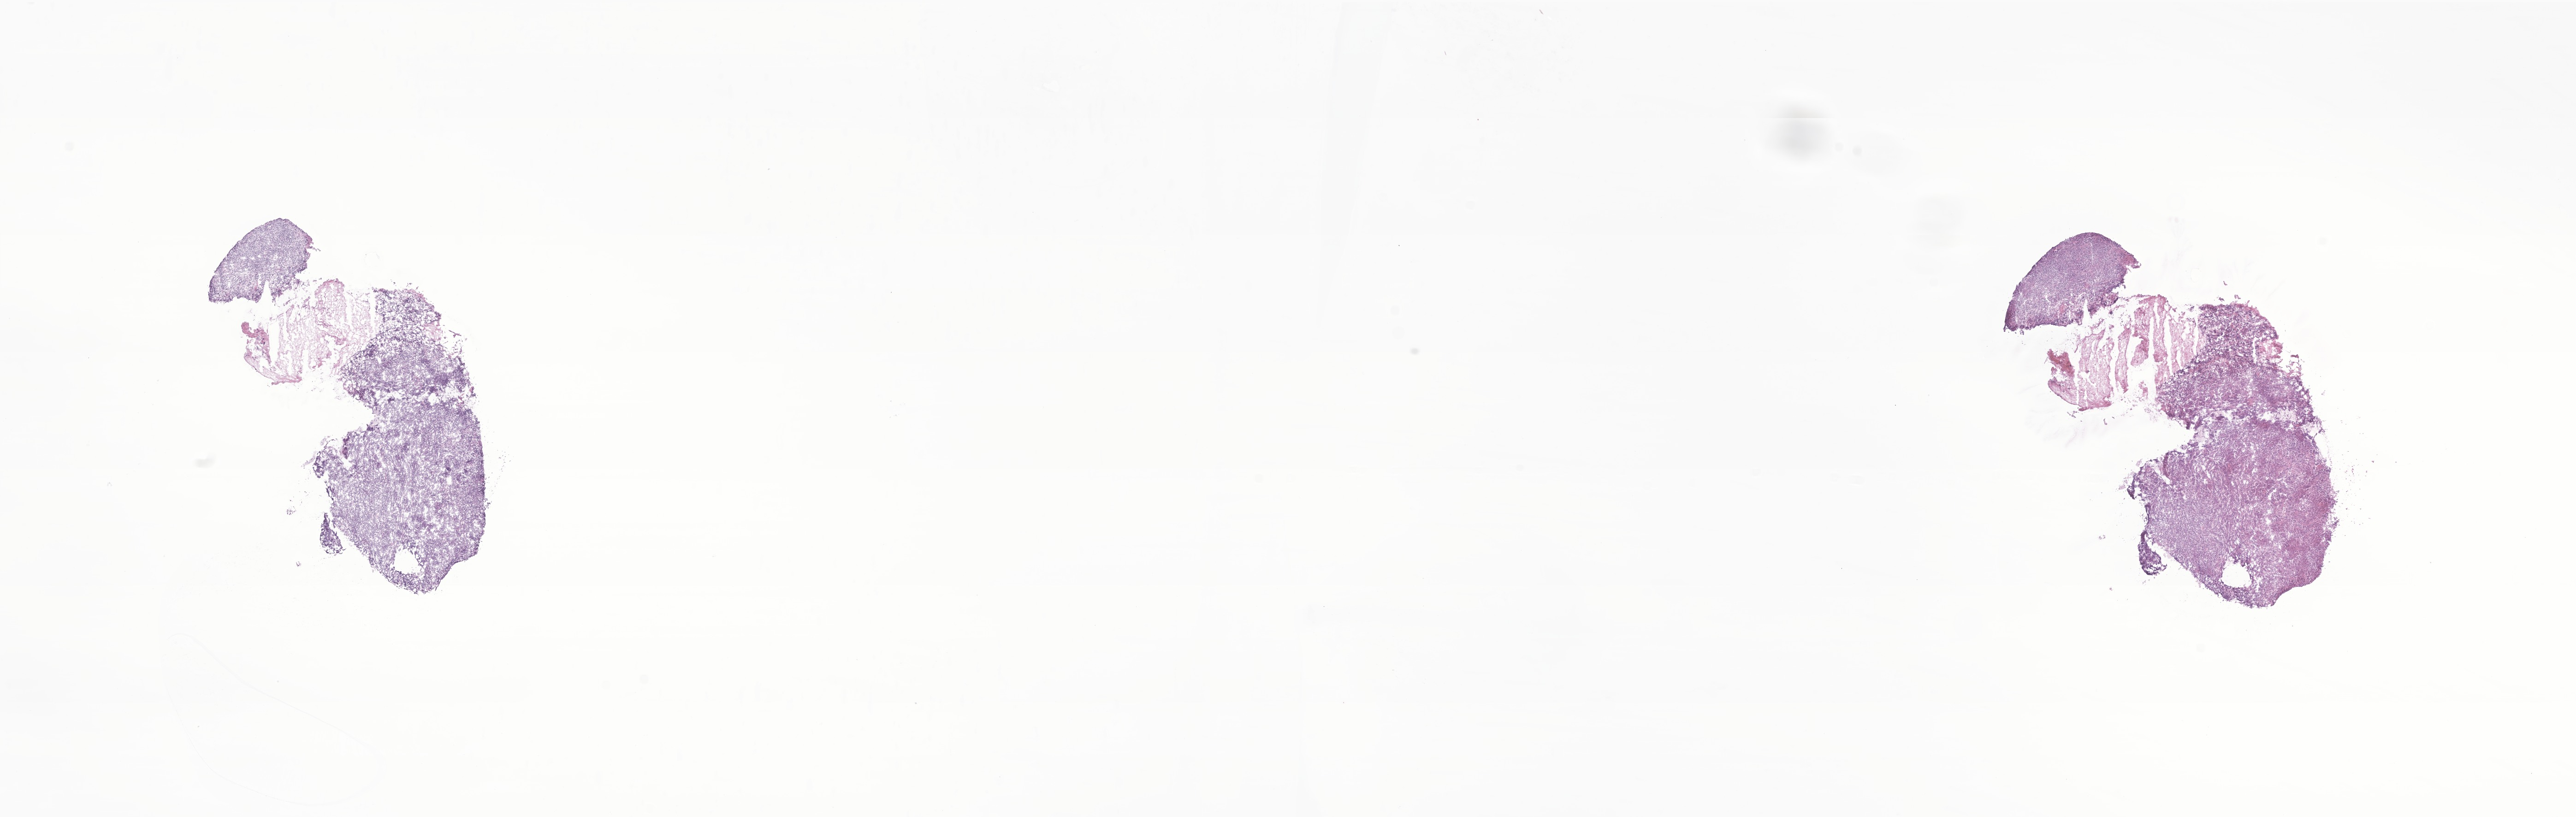
Digitized H&E-stained section of tumor tissue from the brain, shown as a low-resolution overview of the whole scanned area (about 23.6 x 7.5 mm); cryosection (OCT / tissue freezing medium). Patient male; age 186 days.
• diagnosis: Medulloblastoma, NOS